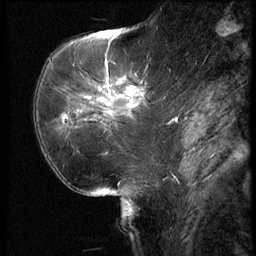
Breast MRI (dynamic contrast-enhanced), one sagittal slice; 3 images stored at this slice position (order not interpretable as contrast timing); 1.5 T; TE 4.2 ms, TR 9 ms; 2.5 mm slice thickness; 256 × 256 image matrix, field of view 180 × 180 mm. Female patient, age 62 years. From the clinical record (not read from this slice): setting: breast cancer imaged before/during neoadjuvant chemotherapy; receptor status: HR-positive, HER2-negative.
Outlined on this slice (semi-automatic segmentation, software-assisted and operator-edited):
- analysis volume of interest (the breast-tissue region the enhancement analysis was run in; not a lesion): bounding box [x1, y1, x2, y2] px = [56, 62, 154, 155]
- tumour enhancement mask (voxels above the 140 % enhancement threshold inside the analysis volume of interest): [63, 89, 134, 119]